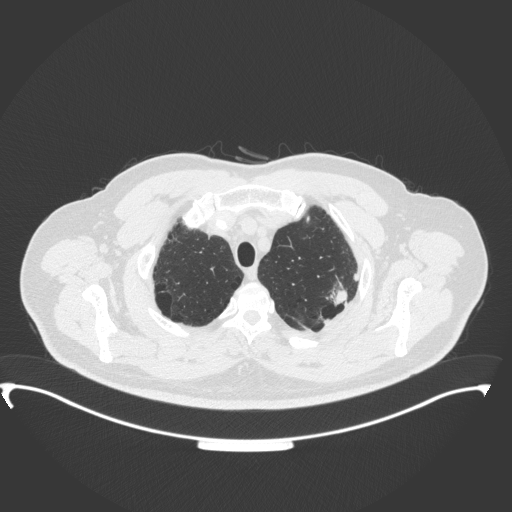
Chest CT, one axial slice; position 314 of 350 along the scan axis; reconstruction kernel B31f; 120 kVp; lung window (W 1500 / L -600 HU); 512 × 512 image matrix, field of view 459 × 459 mm. Male patient, age 64 years. Case-level facts recorded for this patient, not image findings: clinical TNM (as recorded): T1c N1 M1.
Annotated regions visible in this slice (bounding box drawn by a radiologist):
- lung tumour (recorded histology: adenocarcinoma): bounding box (x1, y1, x2, y2) in pixels: (330, 279, 351, 309)